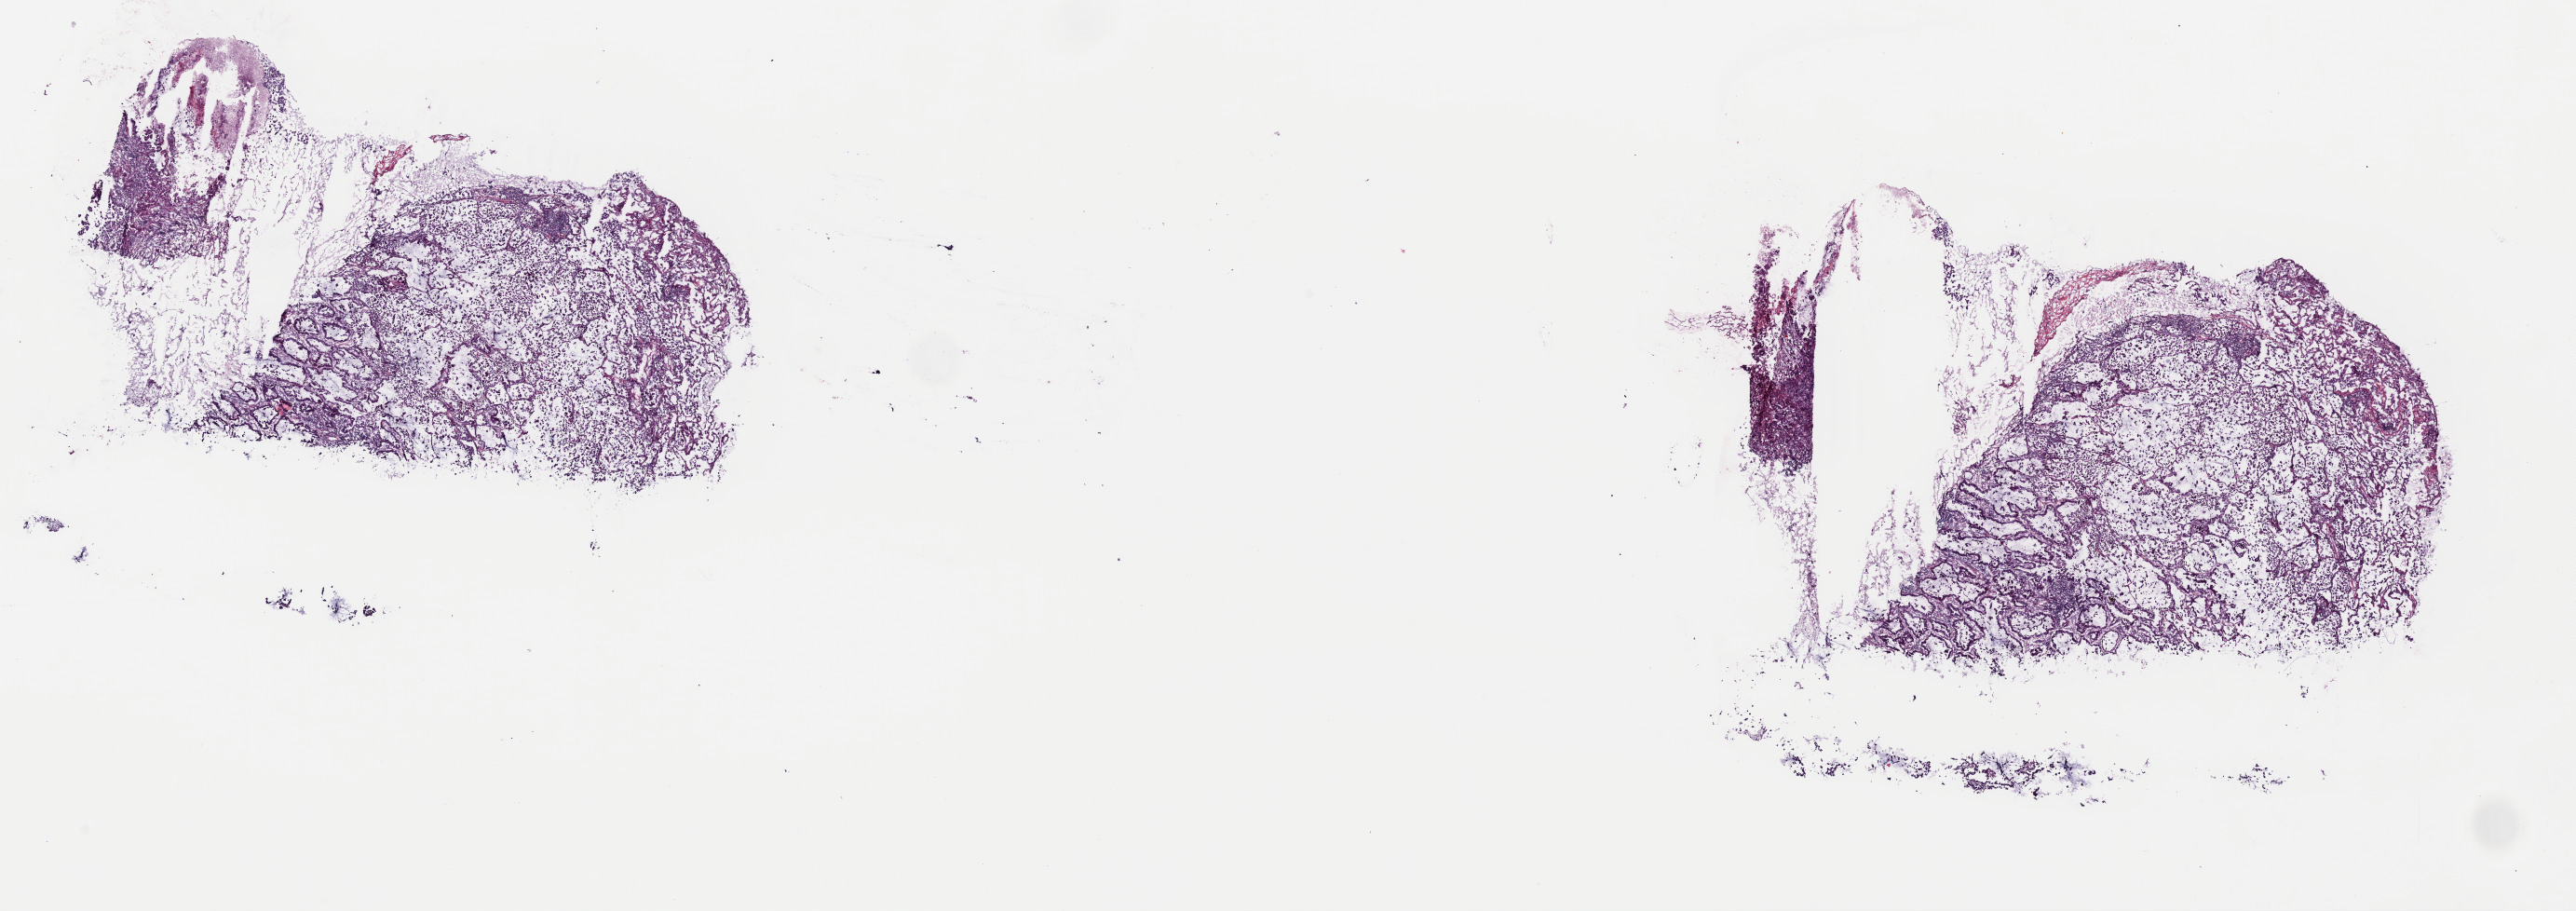
Whole-slide histology image, H&E-stained — whole scanned area (about 21.9 x 7.7 mm) shown as a low-resolution overview; frozen section; lung, primary tumour sample. Patient: female, age at initial diagnosis 74 years. Slide review estimates, as recorded: tumour cells 90%, tumour nuclei 75%, normal cells 0%, stromal cells 0%, necrosis 10%. Infiltration values recorded for this section: lymphocyte infiltration 5%, monocyte infiltration 1%, neutrophil infiltration 1%.
AJCC pathologic stage: IIIA (7th edition). Pathologic diagnosis: Adenocarcinoma with mixed subtypes (upper lobe, lung).